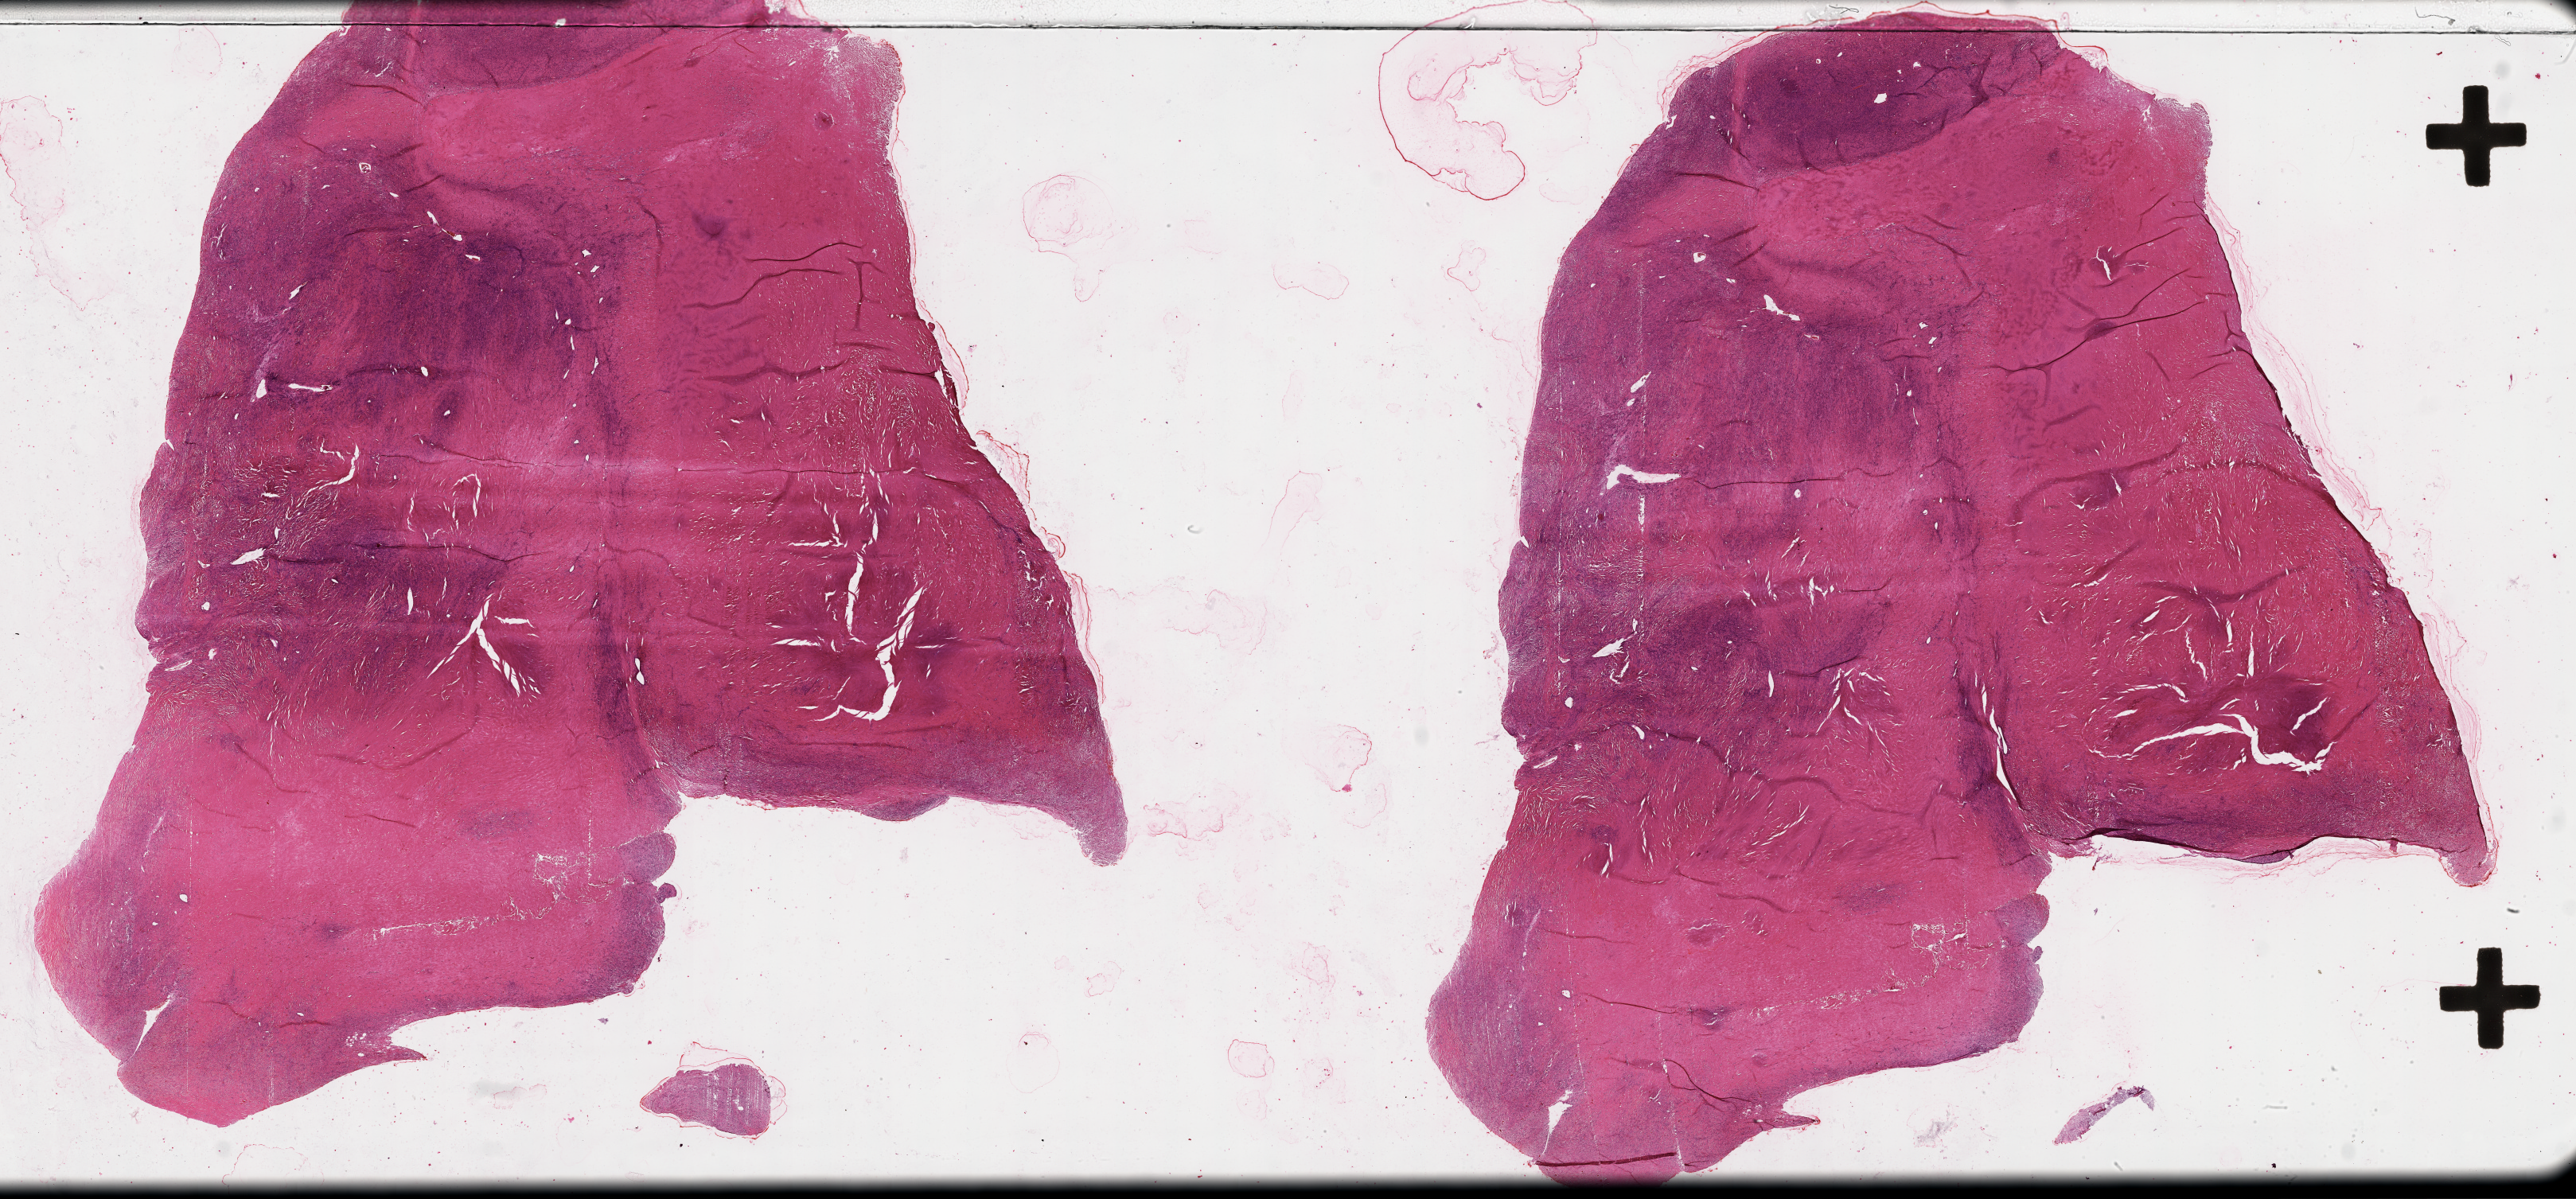
Whole-slide histology image, Hematoxylin and eosin (H&E) stained, shown as a low-resolution overview of the whole scanned area (about 52.1 x 24.3 mm); tumour tissue sample. Male, 62 y/o.
- primary tumour site (as recorded): chest
- patient diagnosis (cohort enrolment): sarcoma (site not recorded at cohort level)